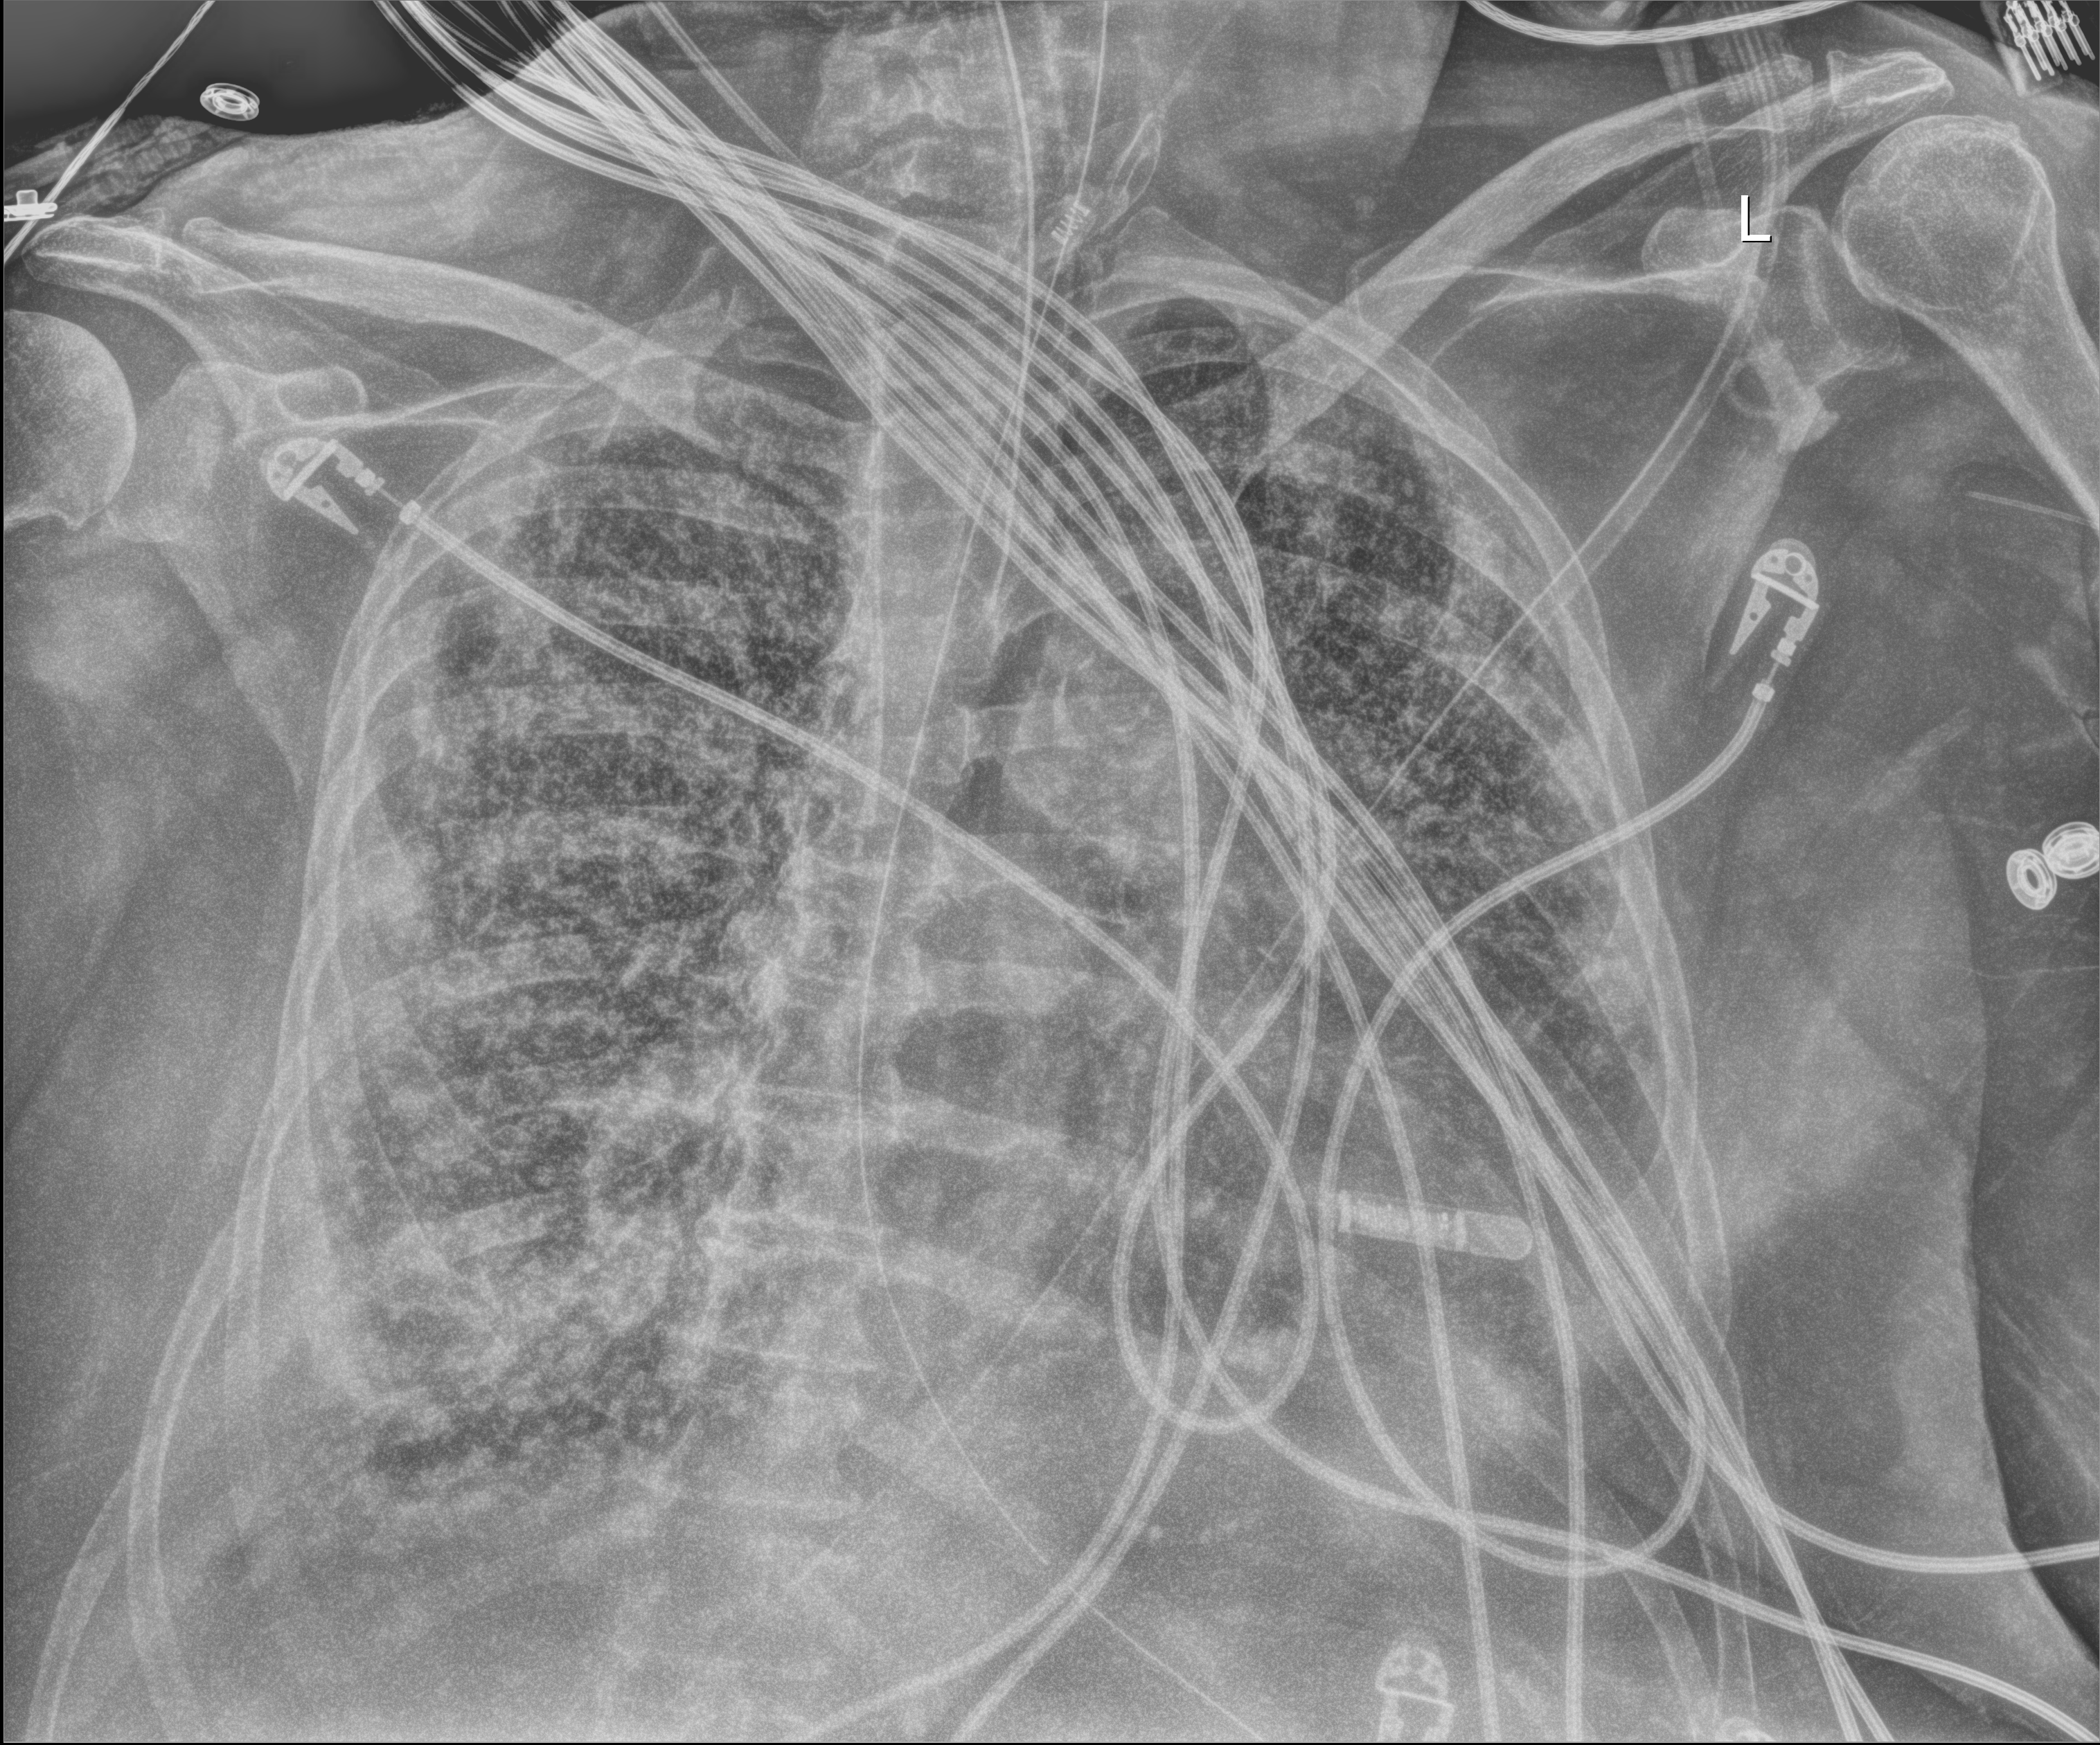
Portable chest radiograph, anteroposterior (AP) projection. Female patient hospitalised with COVID-19, age 60–74 years.
Hospital-stay facts (about this admission, not read from this image; timing relative to this image not recorded):
- admitted to intensive care during this hospital stay: yes
- other chronic lung disease (admission record): yes
- mechanically ventilated during this hospital stay: yes